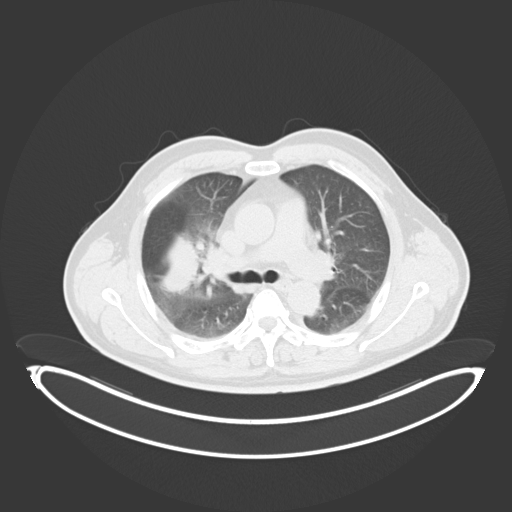
Chest CT, one axial slice. Position 215 of 284 along the scan axis. Reconstruction kernel B30f. 120 kVp. Lung window (W 1500 / L -600 HU). 3 mm slice thickness. 512 × 512 image matrix. Patient: male, 55 years. Case-level facts recorded for this patient, not image findings: clinical TNM (as recorded): T3 N2 M1.
Outlined on this slice (bounding box drawn by a radiologist):
- lung tumour (recorded histology: adenocarcinoma): bounding box (x1, y1, x2, y2) in pixels: (151, 230, 208, 297)